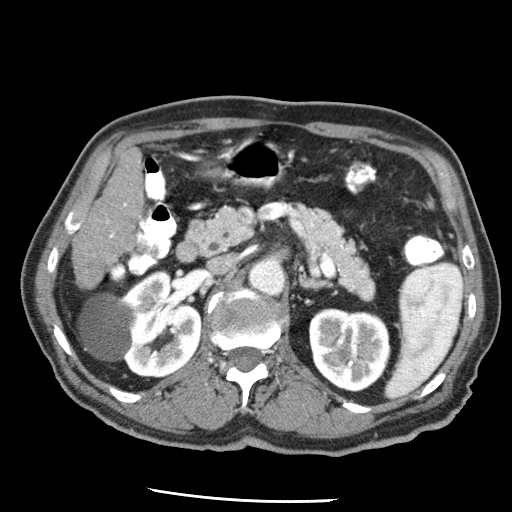
Contrast-enhanced abdominal CT (liver protocol), one axial slice. Slice 16 of 79 in the series (ordered by position). Reconstruction kernel STANDARD. Soft-tissue window (W 400 / L 40 HU). 2.5 mm slice thickness. 512 × 512 image matrix, field of view 320 × 320 mm. From the clinical record (not read from this slice): diagnosis: hepatocellular carcinoma (patient treated with transarterial chemoembolisation; whether this scan precedes or follows treatment is not stated here); TNM stage (as recorded): Stage-IIIA; Child-Pugh class: A; tumour differentiation: moderately differentiated; tumour size: 7 cm.
Annotated regions visible in this slice (semi-automatic segmentation, software-assisted and operator-edited):
- liver parenchyma outside the tumour (the mass and vessels are separate outlines, so this box may not span the whole liver): bounding box <90,148,144,251> (left, top, right, bottom; pixels)
- liver vessels: <110,203,126,238>